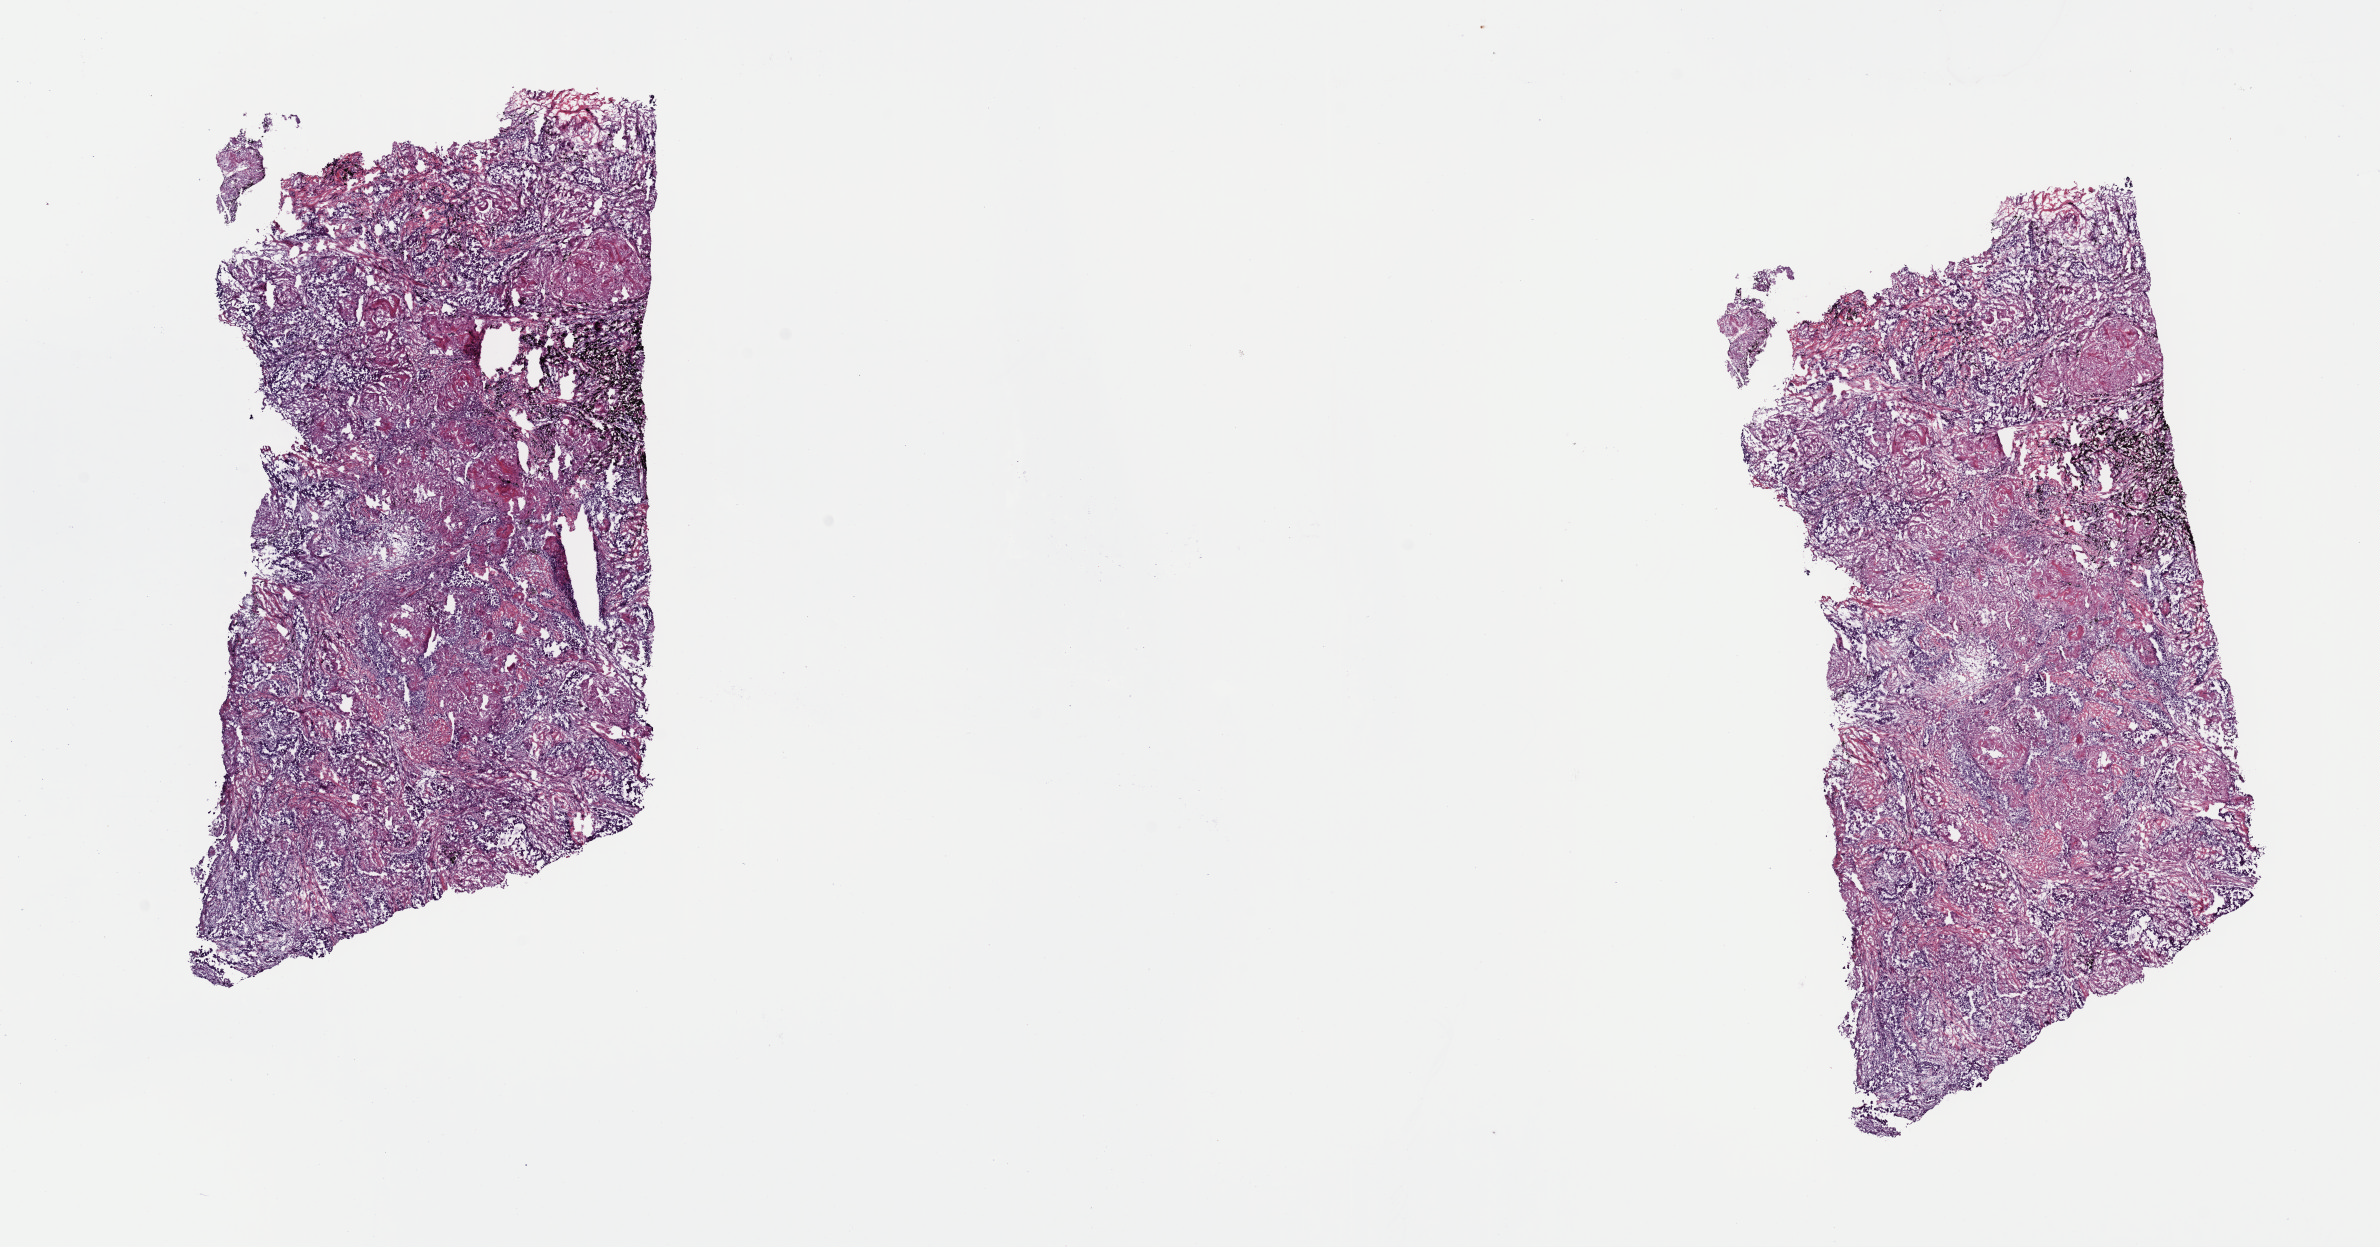
Digitized H&E tissue section (whole slide) — shown as a low-resolution overview of the whole scanned area (about 18.8 x 9.8 mm, acquisition: 40x scan); frozen section; sample: primary tumour, lung. Patient: male, age at initial diagnosis 61 years. Slide review estimates, as recorded: tumour cells 95%, tumour nuclei 65%, normal cells 0%, stromal cells 5%, necrosis 0%. Infiltration values recorded for this section: lymphocyte infiltration 0%, monocyte infiltration 0%, neutrophil infiltration 0%.
Histologic diagnosis: Adenocarcinoma, NOS. AJCC pathologic stage: IIB (5th edition). Laterality: right. TNM: T2 N1 M0.